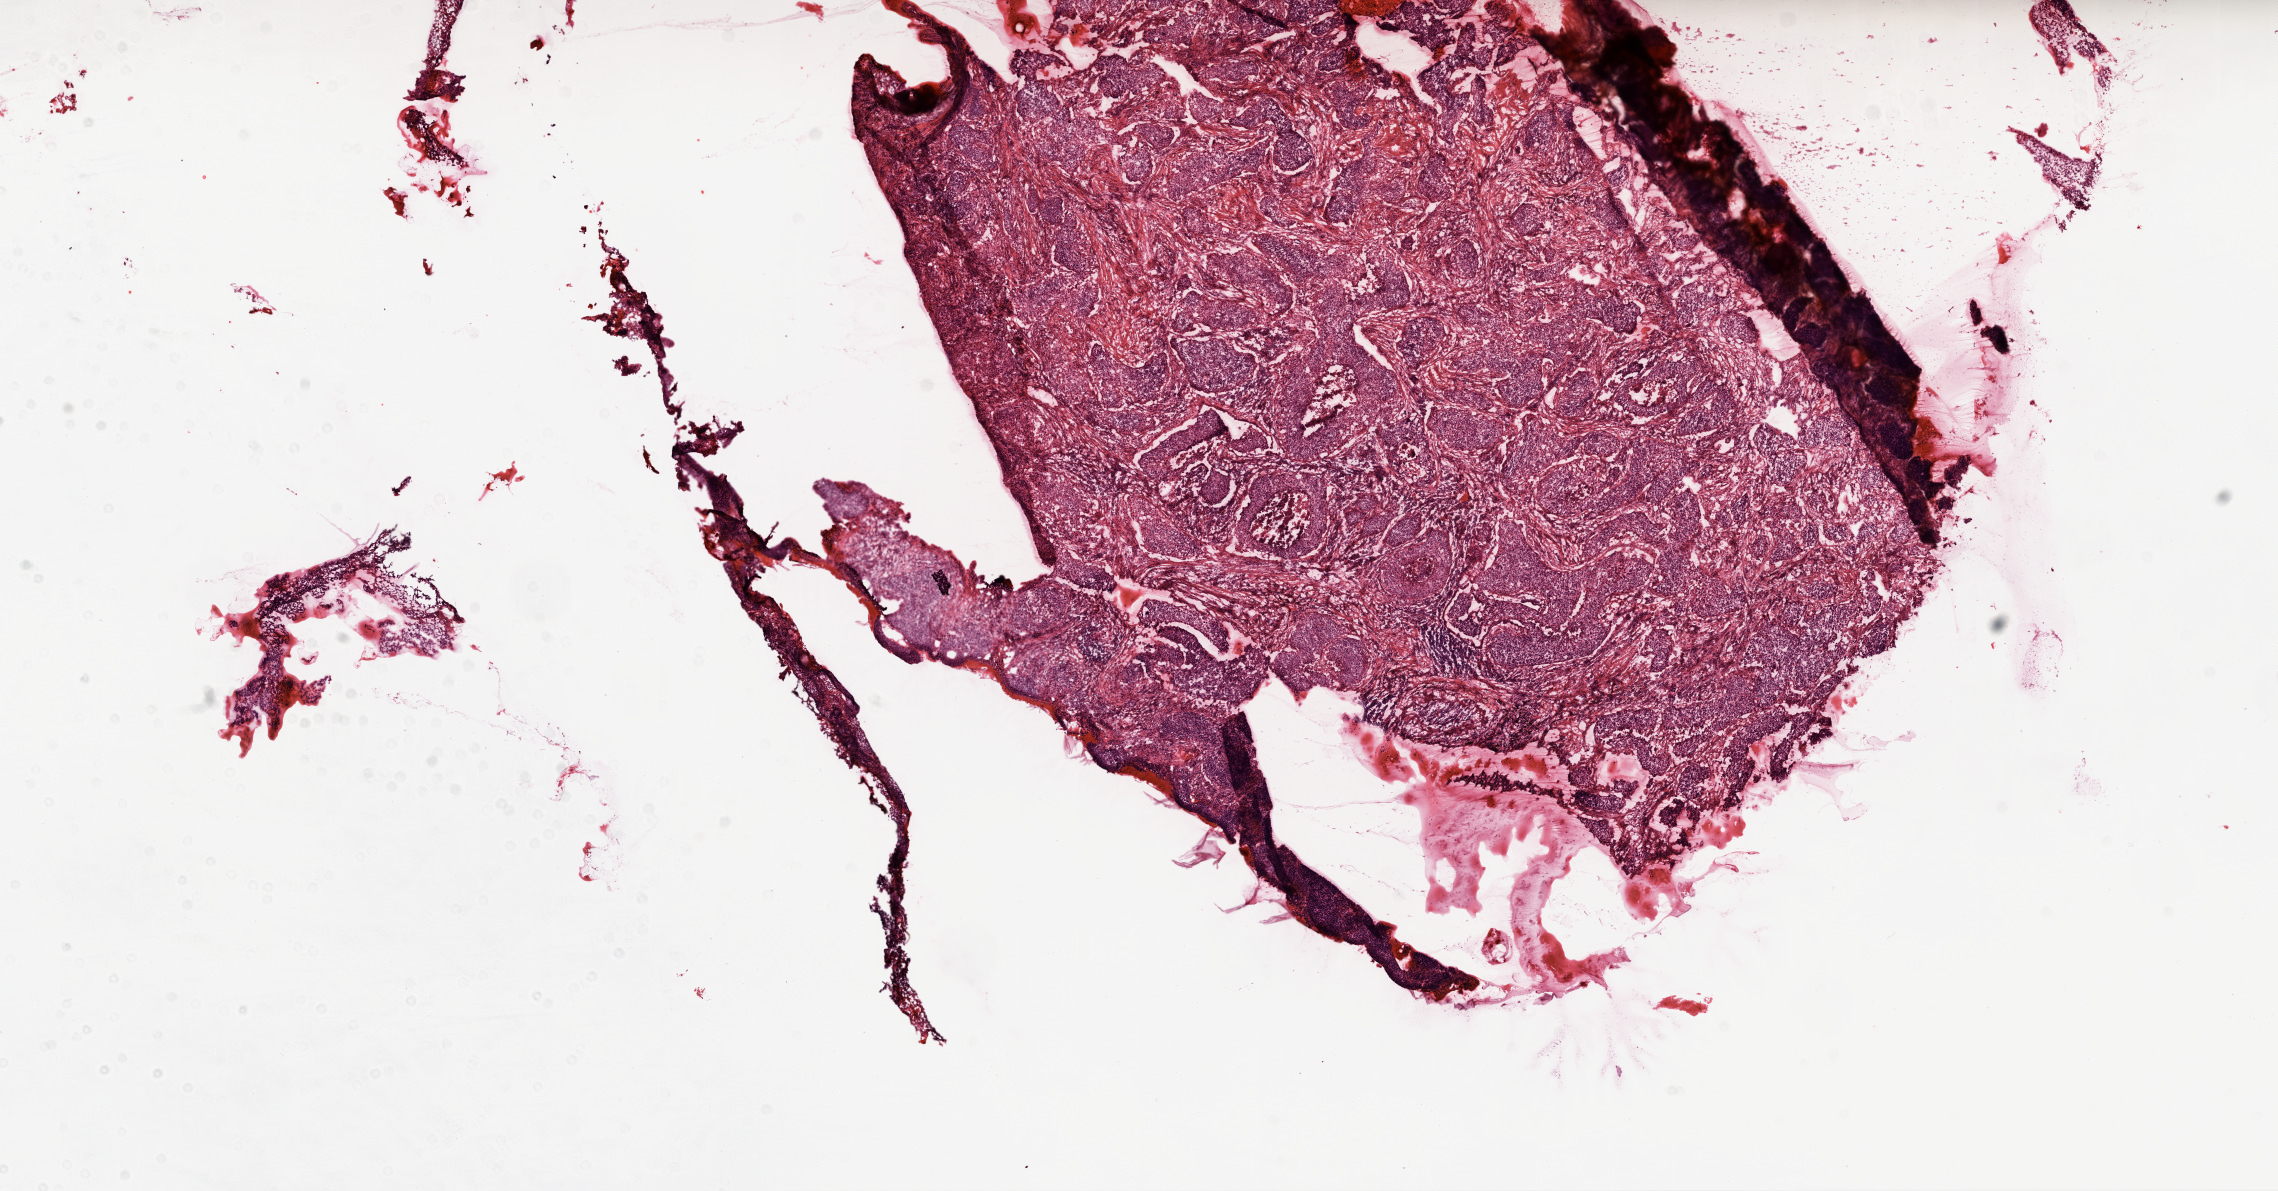
Digitized H&E-stained tissue section (whole slide), low-resolution overview of the scanned area, about 18.4 x 9.6 mm; frozen section from the top of the tissue portion; lung, primary tumour sample. Male, age 61 years at initial diagnosis. Pathologist review of this section (percent, as recorded): tumour nuclei 90%, necrosis 0%.
Histologic diagnosis: Squamous cell carcinoma, NOS (lower lobe, lung). Laterality: left. AJCC pathologic stage: IB.